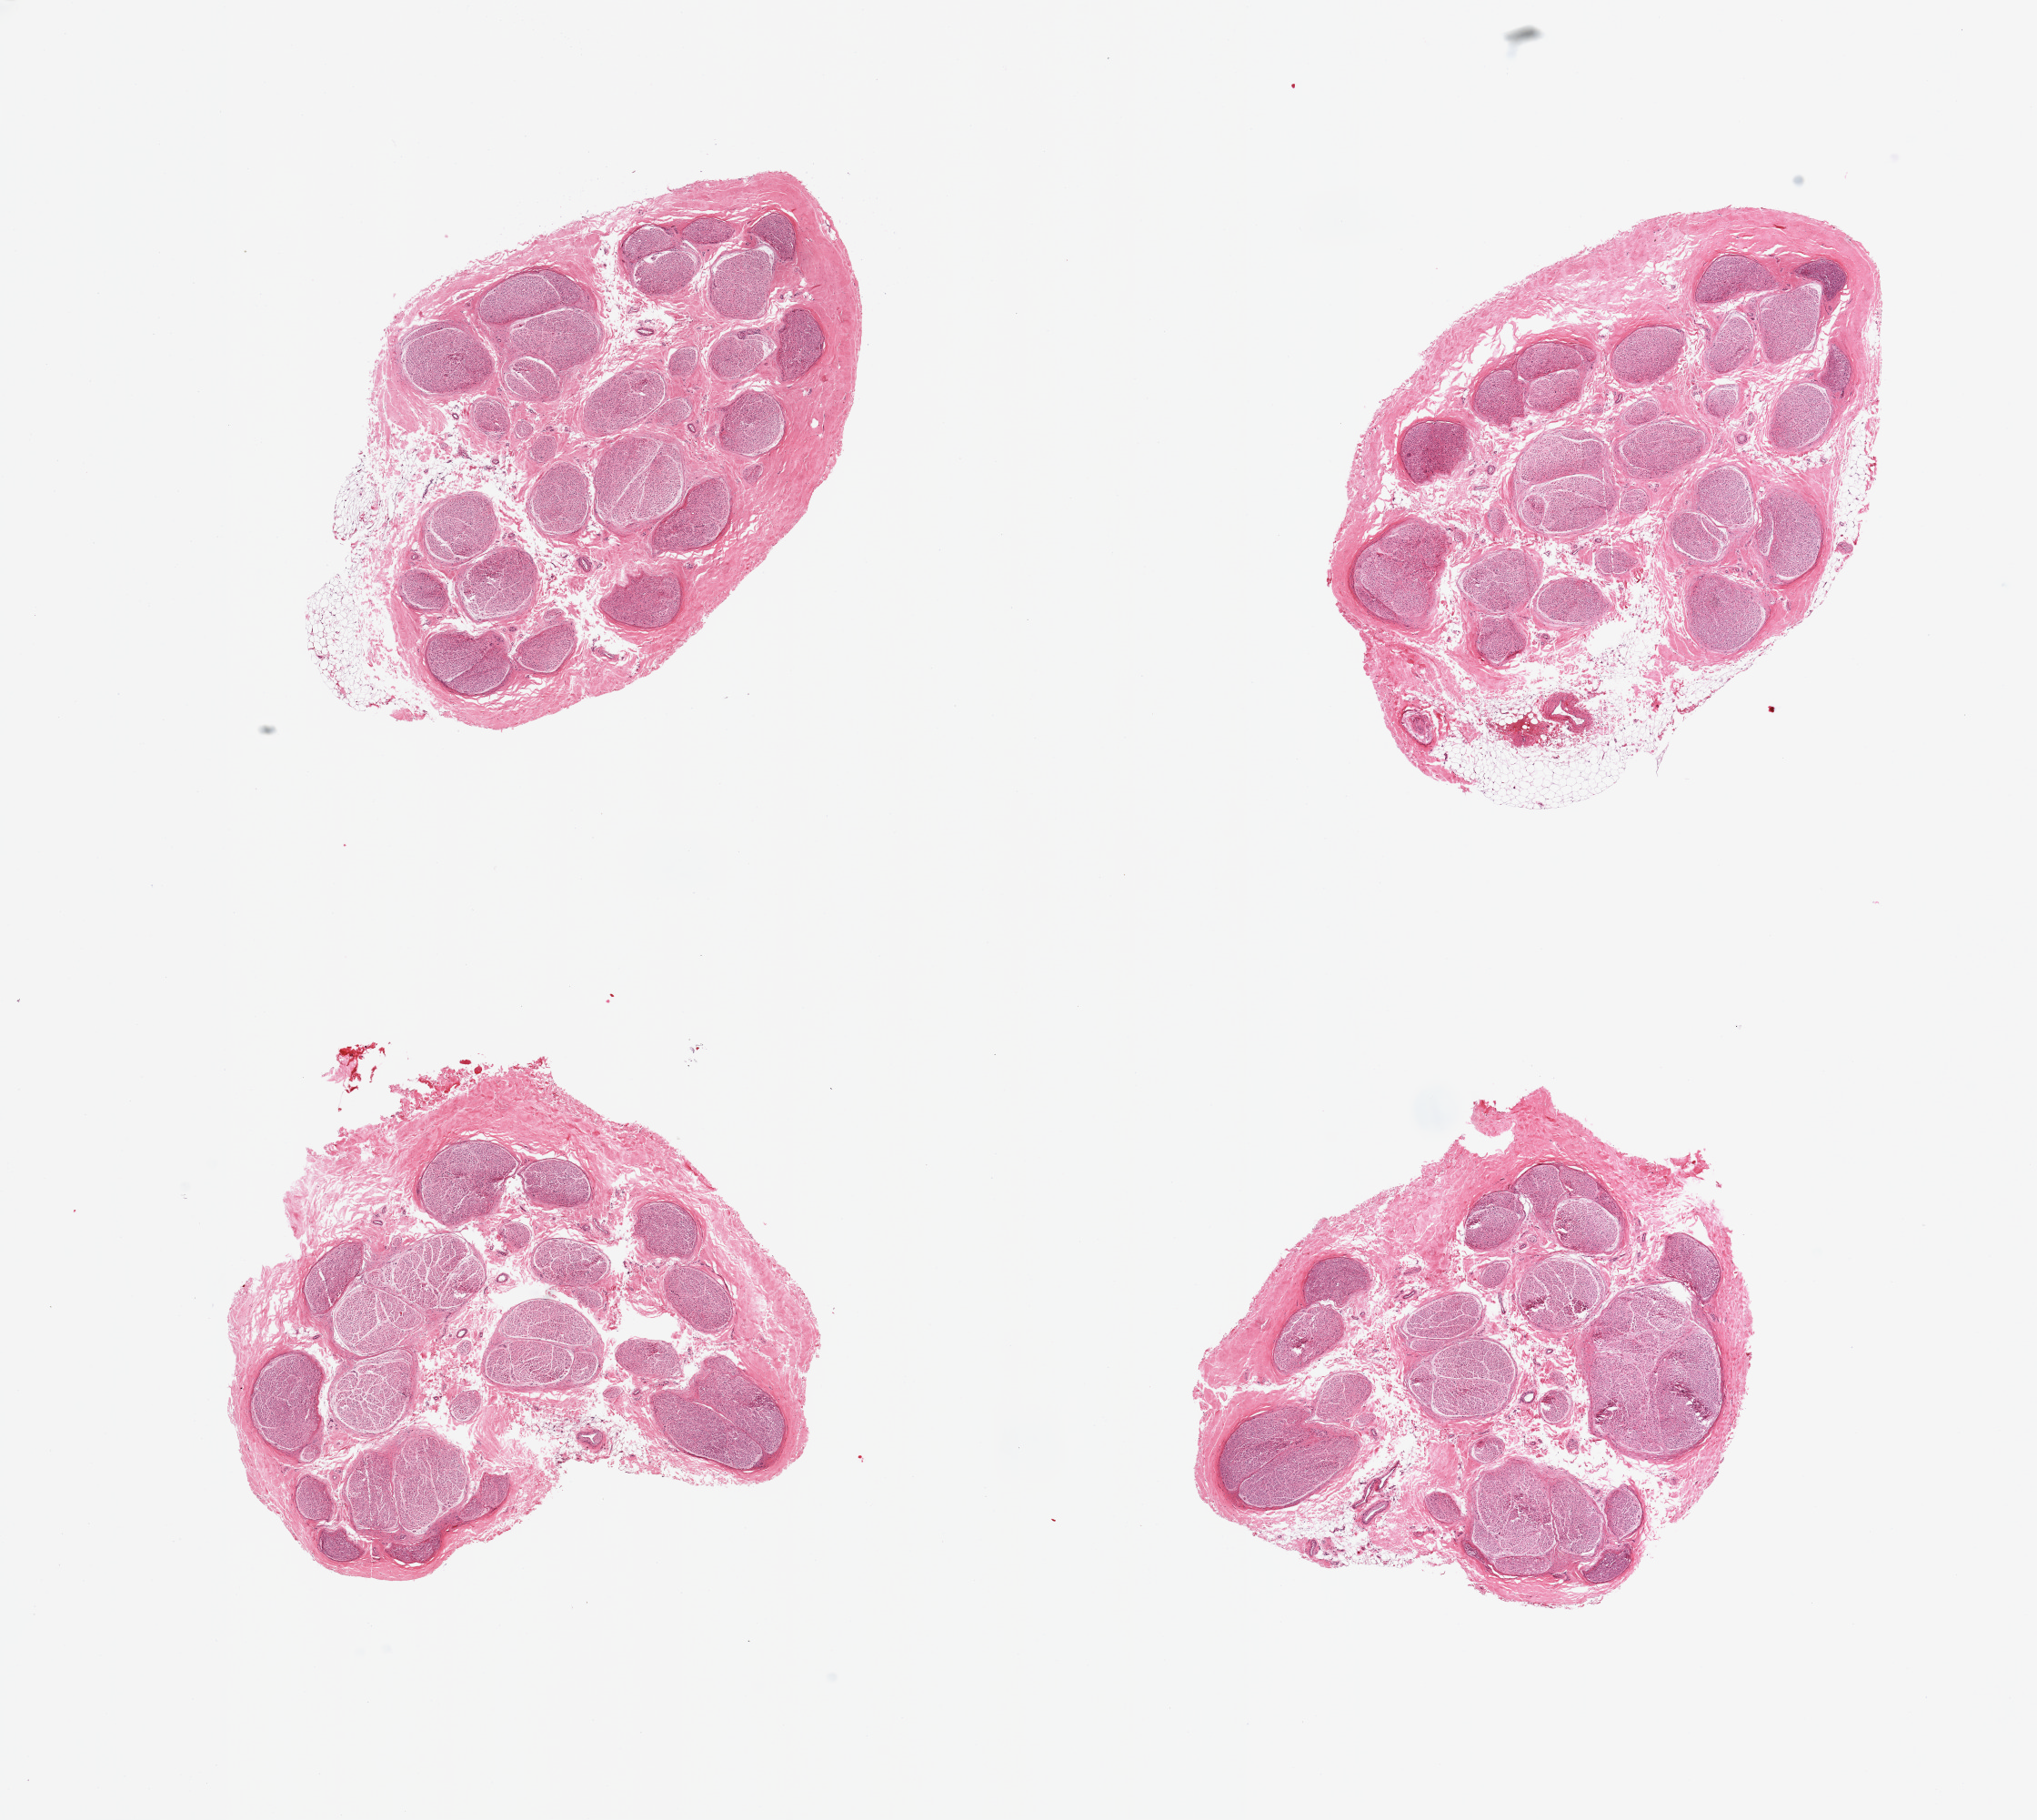
Whole-slide image, H&E stain — a low-resolution overview of the entire scanned area, about 17.7 x 15.8 mm; PAXgene-fixed, paraffin-embedded tissue; target tissue: tibial nerve; donor tissue sample. Donor: male.
* reviewer comment on this tissue sample: 4 pieces; up to ~15% internal/external fat